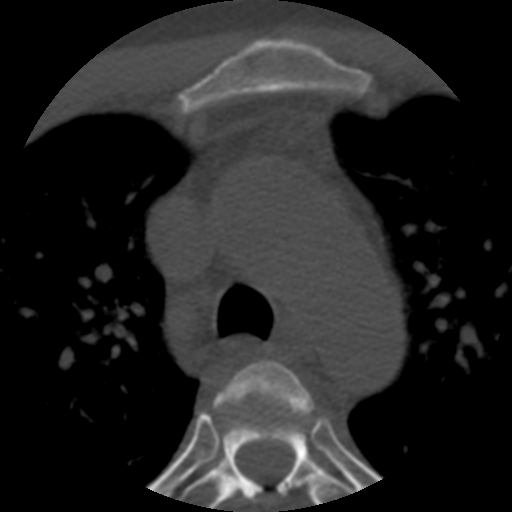
CT including the spine, one axial slice. Position 402 of 508 along the scan axis. Reconstruction kernel STANDARD. 120 kVp. Bone window (W 1800 / L 400 HU). 1.25 mm slice thickness. 512 × 512 image matrix, field of view 160 × 160 mm. Patient age 57 years. From the clinical record (not read from this slice): primary cancer: prostate.
Annotated regions visible in this slice (semi-automatically segmented with operator editing):
- T3 vertebra: box from (x=214, y=360) to (x=314, y=503) px
- T4 vertebra: (x=179, y=422)–(x=355, y=512)